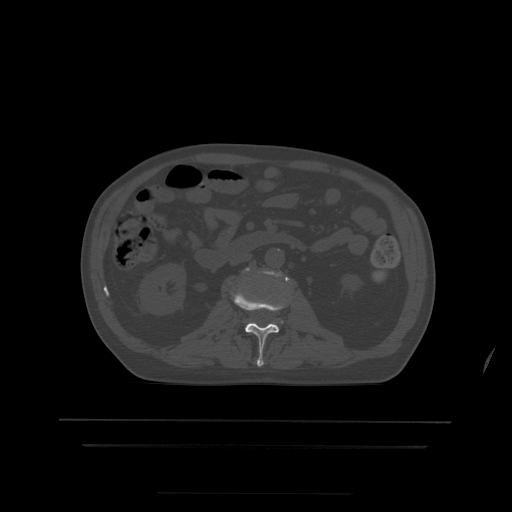
CT including the spine, one axial slice; position 138 of 522 along the scan axis; bone window (W 1800 / L 400 HU); 1.25 mm slice thickness; 512 × 512 image matrix, field of view 436 × 436 mm. Patient age 68 years. From the clinical record (not read from this slice): primary cancer: urothelial.
Outlined on this slice (semi-automatically segmented with operator editing):
- L2 vertebra: bounding box <232,292,284,367> (left, top, right, bottom; pixels)
- L3 vertebra: <246,269,289,306>